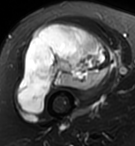
MRI of an extremity soft-tissue mass, one axial slice; position 62 of 95 along the scan axis; T2-weighted fat-saturated; MR volume resampled by the dataset authors to the PET/CT grid (not the native acquisition matrix); 135 × 146 image matrix, field of view 132 × 143 mm. Female patient. Case-level facts recorded for this patient, not image findings: histological type: pleiomorphic undifferentiated sarcoma; grade: high; site of the primary tumour: right quadricep.
Outlined on this slice (expert contour drawn on MRI and transferred to this co-registered scan by the dataset authors):
- gross tumour volume including surrounding oedema: bounding box <16,24,115,115> (left, top, right, bottom; pixels)
- gross tumour volume (mass): <16,24,115,115>